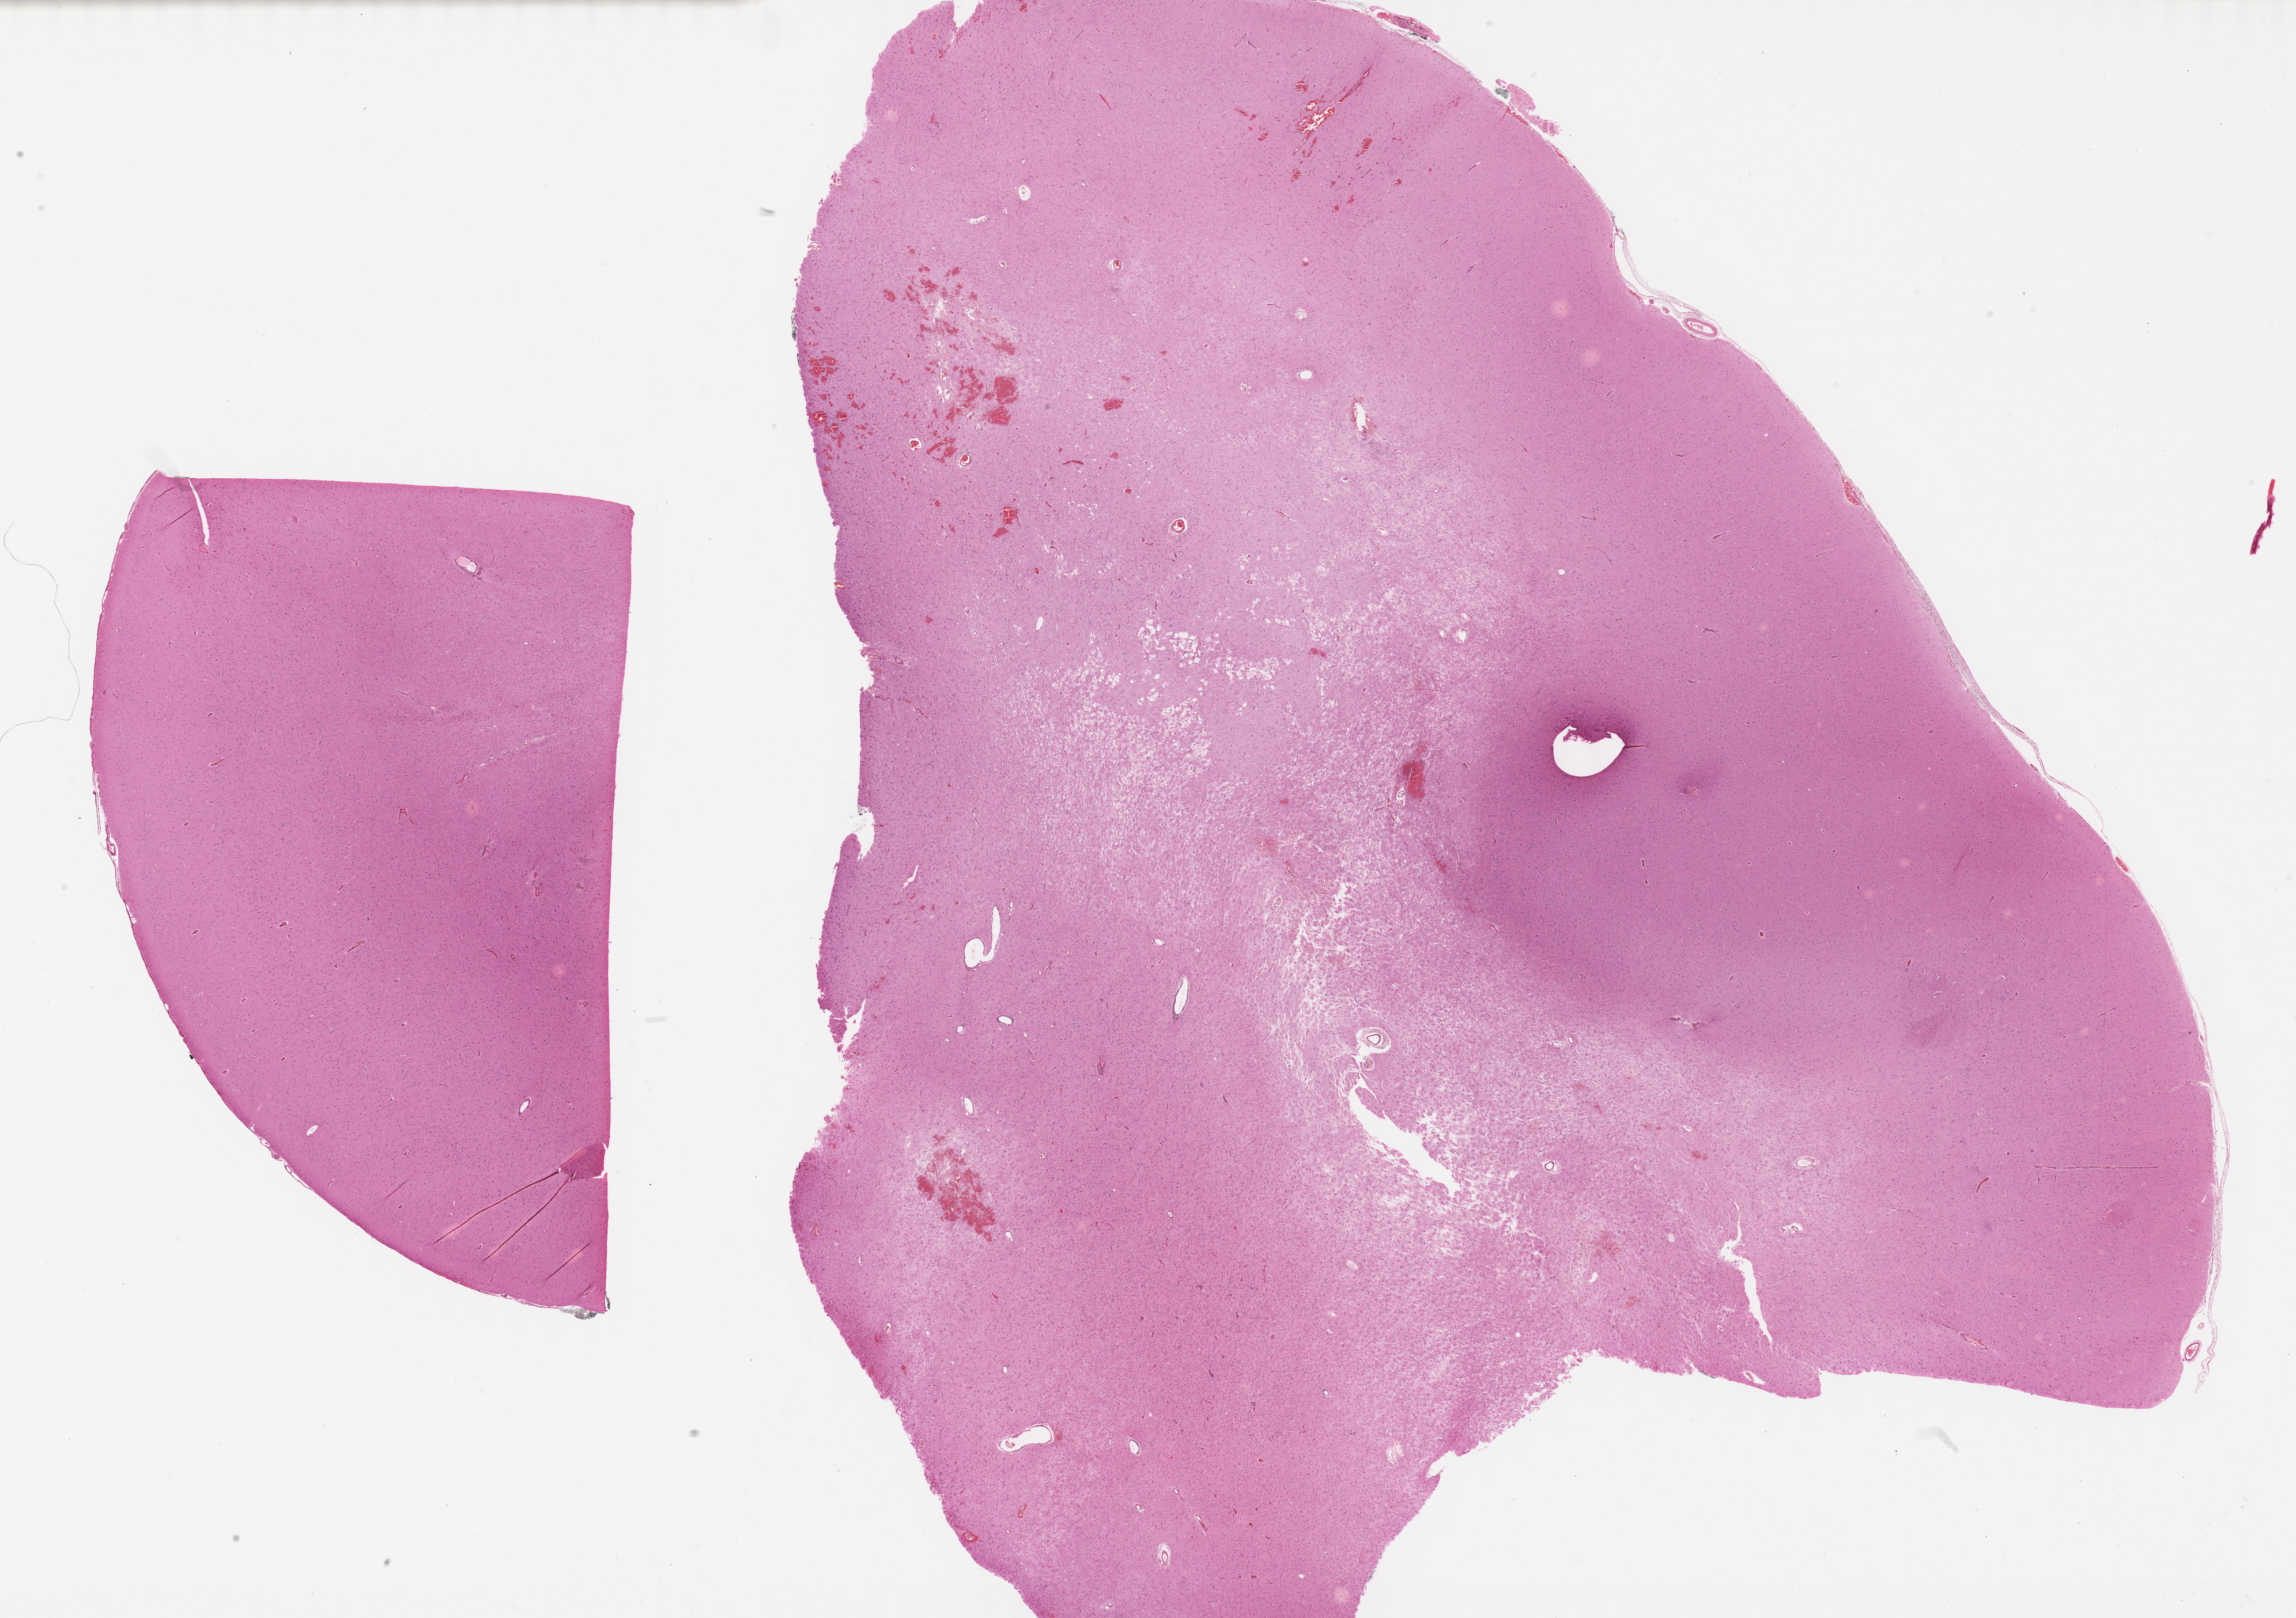
Hematoxylin and eosin (H&E) stained whole-slide image — a low-resolution overview of the entire scanned area, about 32.2 x 22.7 mm (acquisition: 40x scan). Formalin-fixed paraffin-embedded (FFPE) diagnostic section. Brain, primary tumour sample. Male patient; age at initial diagnosis 66 years. Histologic grade: G2 (moderately differentiated).
Pathologic diagnosis: Mixed glioma (cerebrum).